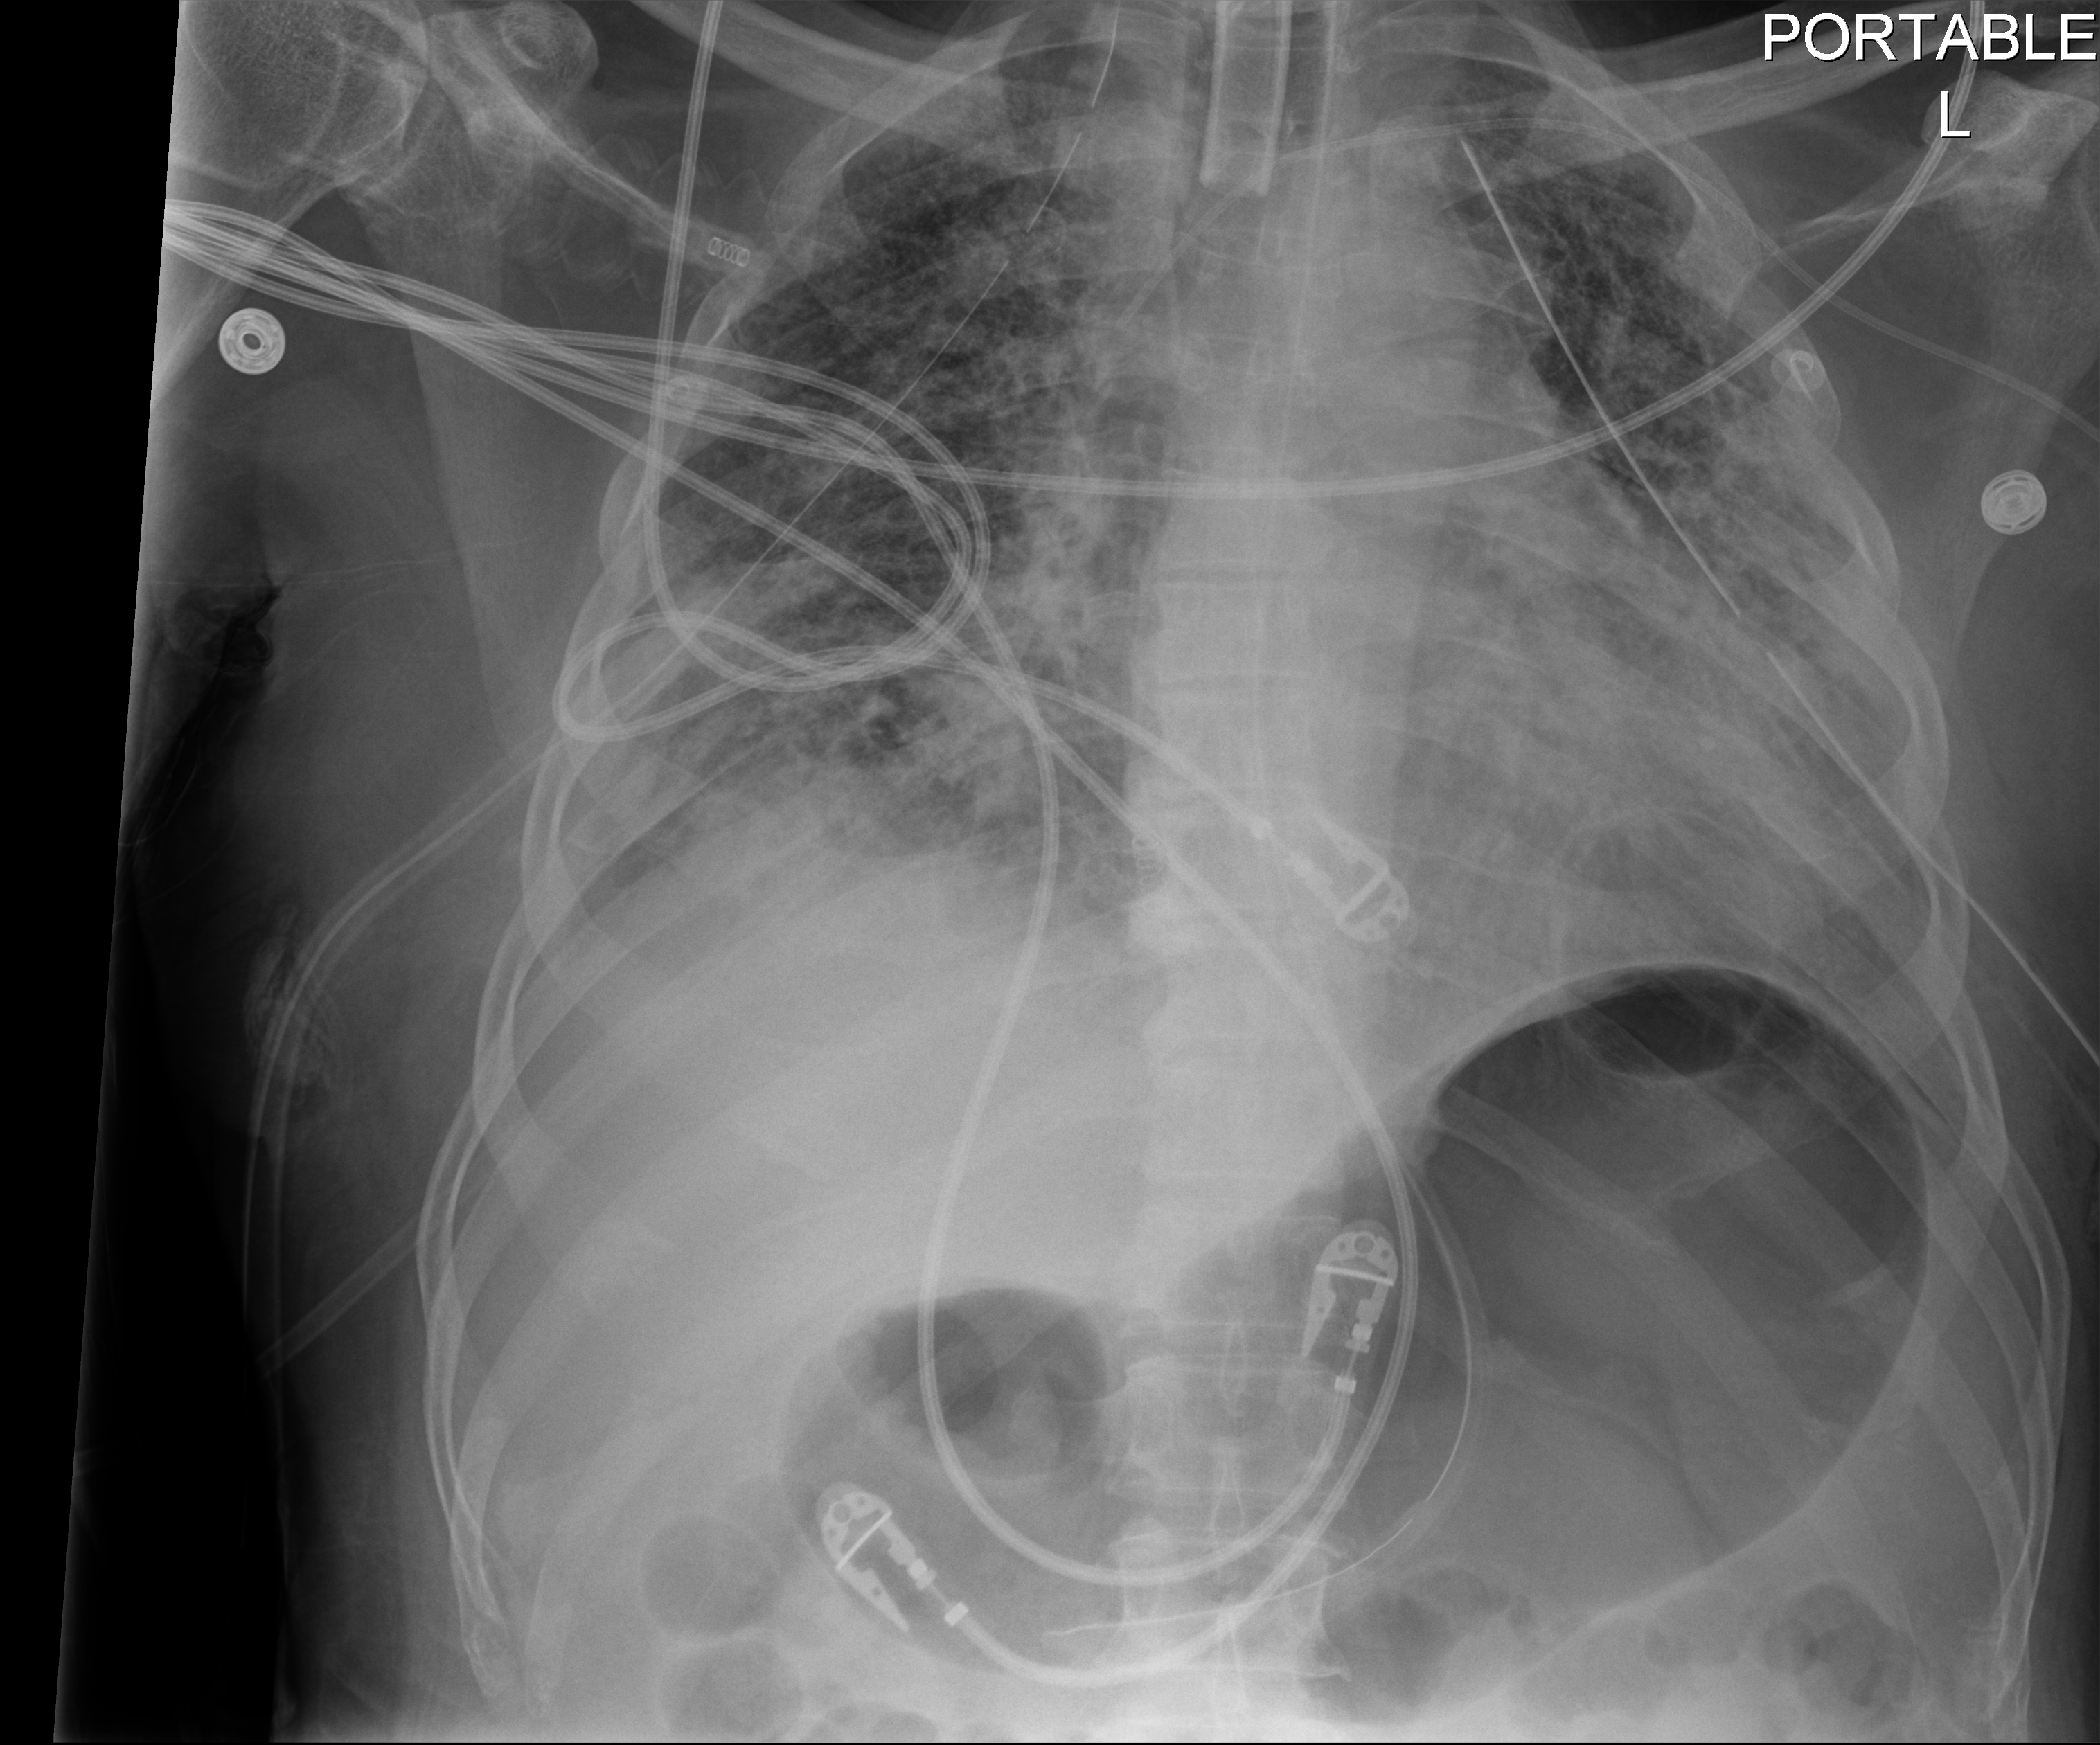
Portable chest radiograph. Patient hospitalised with COVID-19; male, aged 18–59 years.
Hospital-stay facts (about this admission, not read from this image; timing relative to this image not recorded):
- COPD (admission record): no